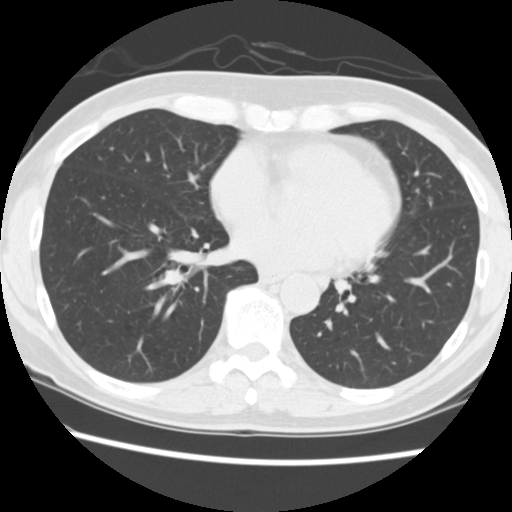
Axial slice from a low-dose chest CT screening exam, second screening round (one year after baseline), lung window (W 1500 / L -600 HU), 2.5 mm slice thickness. Female, age 60 years at enrolment.
Expert-annotated lung lesion, bounding box (x1, y1, x2, y2) in pixels: (413, 185, 446, 219). No non-calcified nodule or mass ≥4 mm was recorded by the screening reader at this exam. Participant outcome: lung cancer diagnosed 509 days after this screen (after the third annual screen) — adenocarcinoma, NOS, lingula, poorly differentiated (G3), stage IA (AJCC 6th edition), 6 mm at pathology.